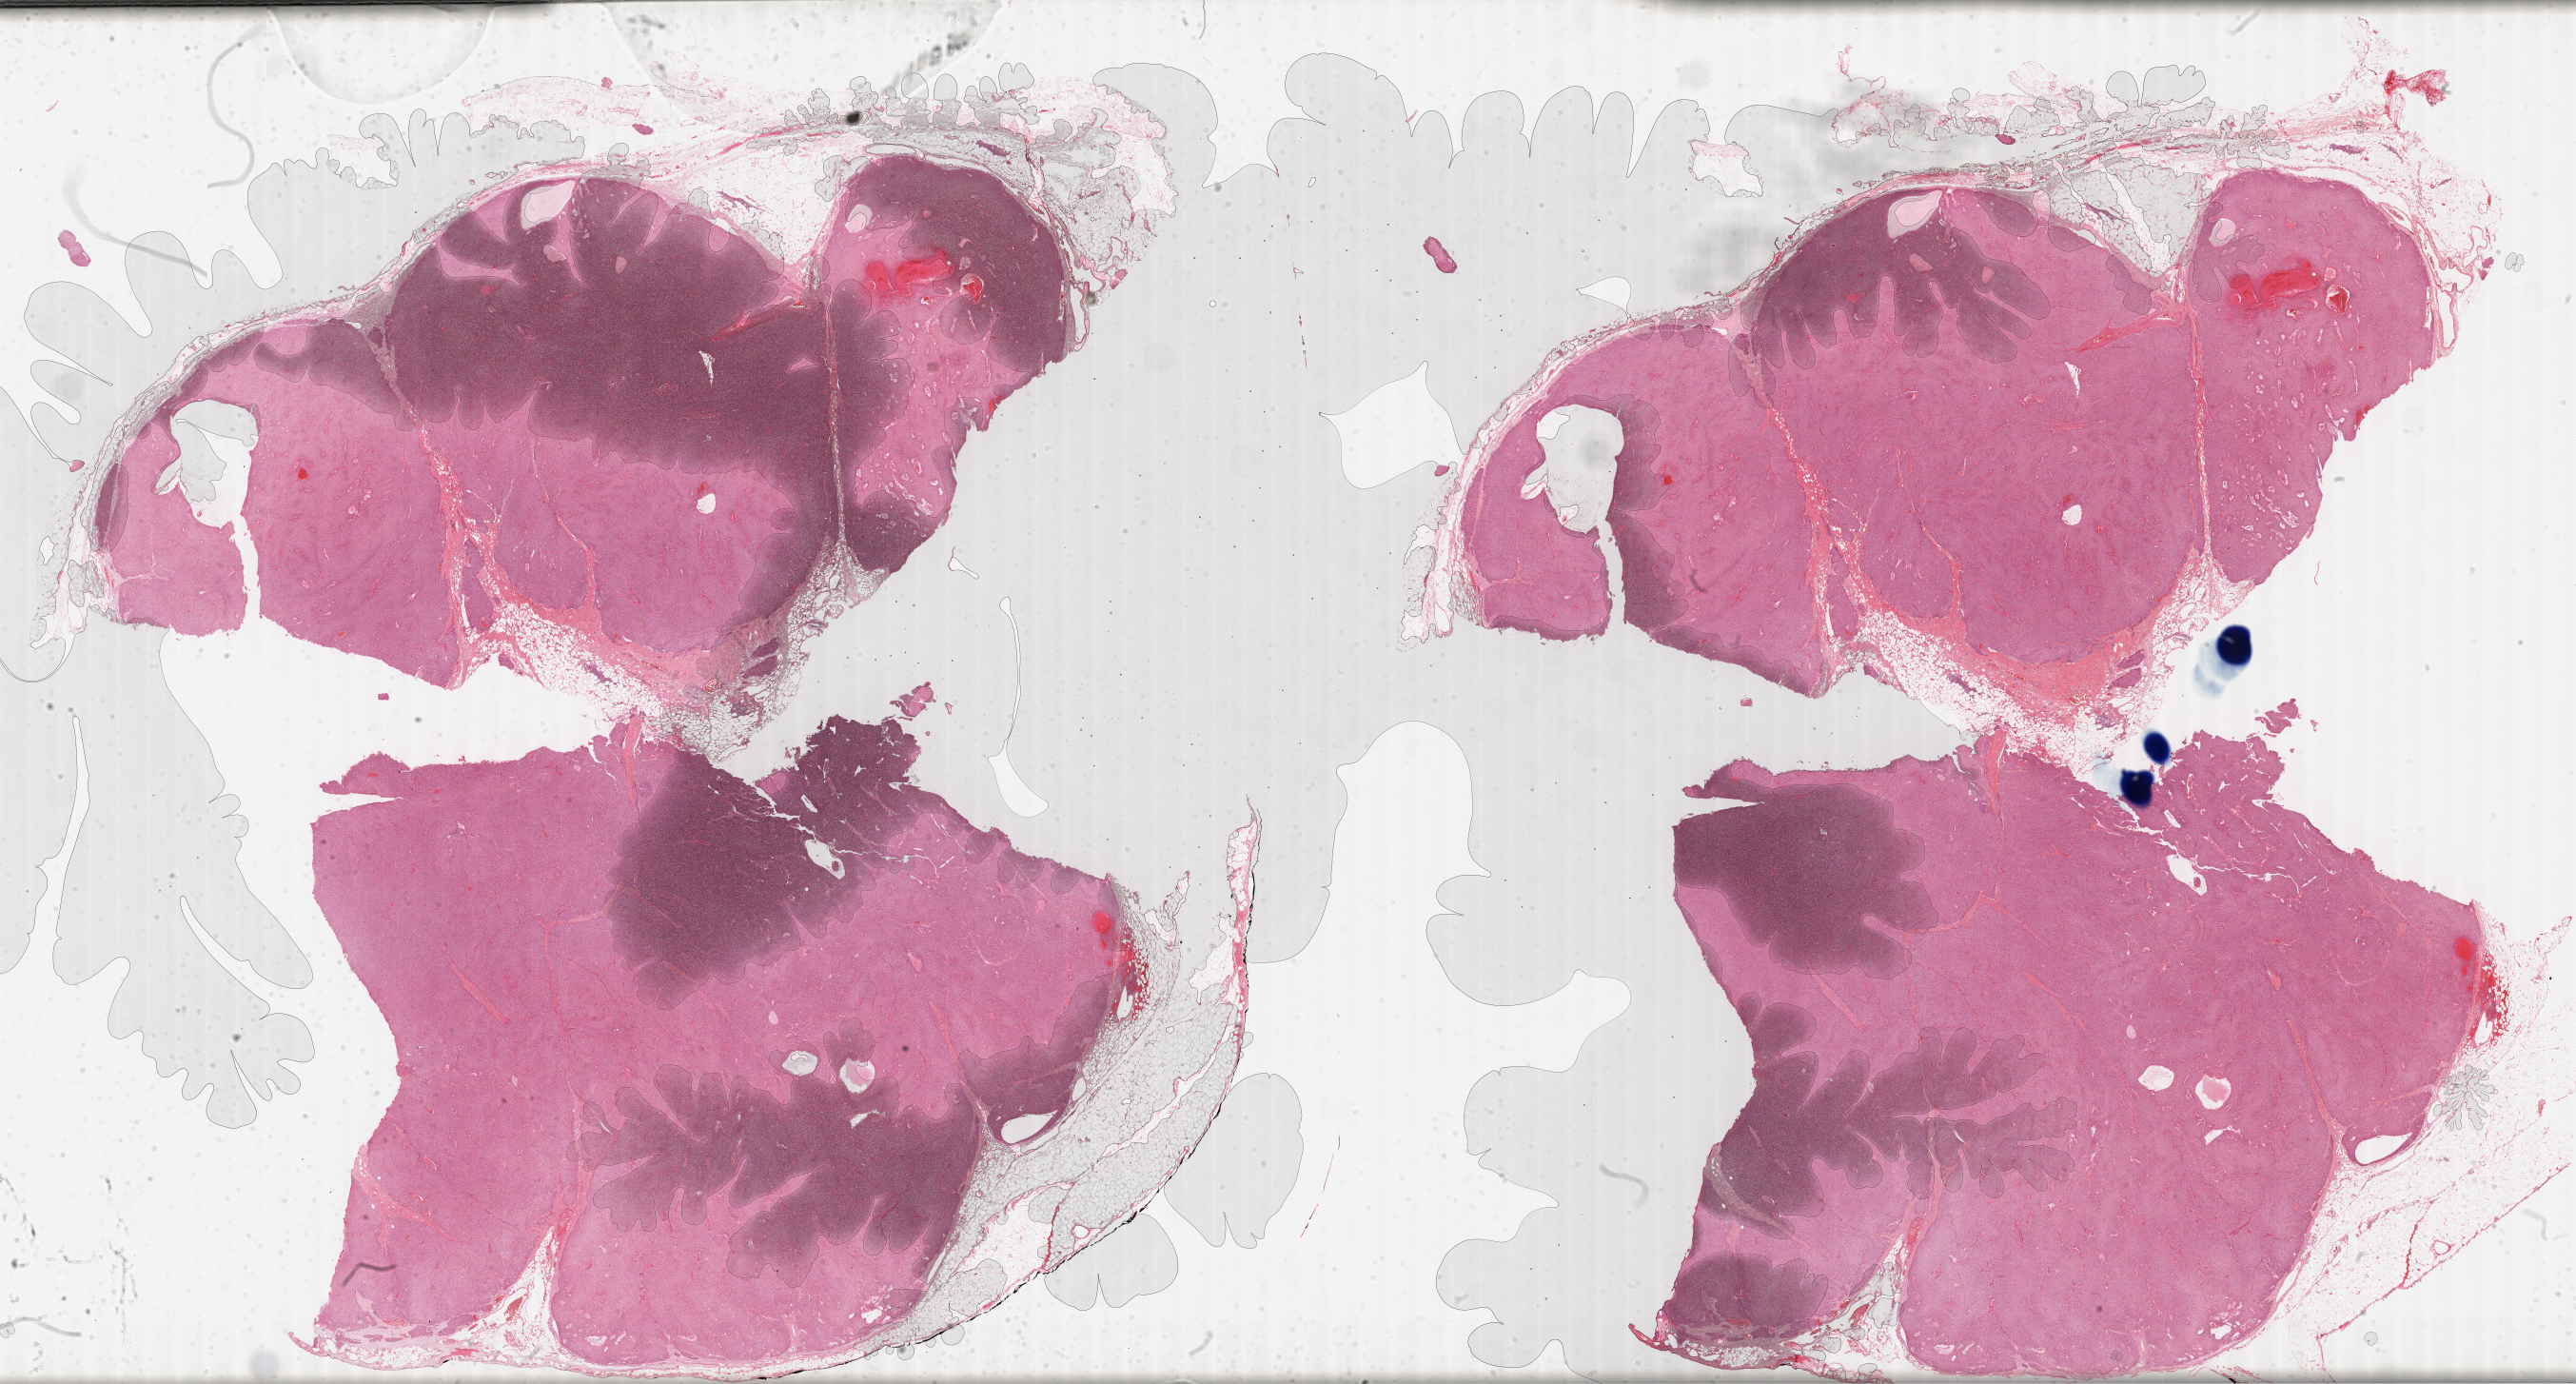
Whole-slide histology image, Hematoxylin and eosin (H&E) stained, whole scanned area (about 43.8 x 23.5 mm) shown as a low-resolution overview. Formalin-fixed paraffin-embedded (FFPE) diagnostic section. Sample: primary tumour, thymus. Female, age 65 years at initial diagnosis.
Diagnosis: Thymoma, type B3, malignant.